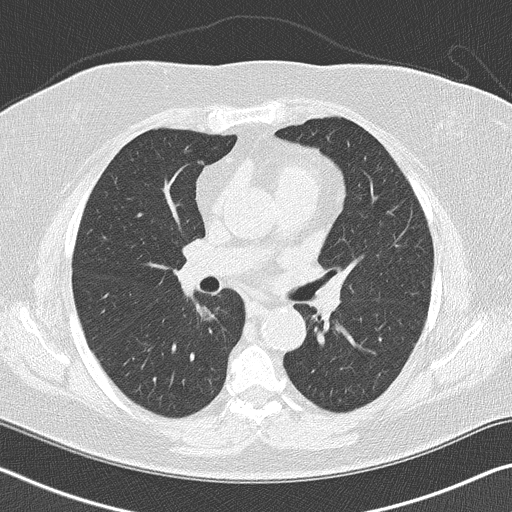
Axial slice from a low-dose chest CT screening exam. First (baseline) screen. Lung window (W 1500 / L -600 HU). 2 mm slice thickness. Female participant, aged 60 years at enrolment.
Expert-annotated lung lesion, box from (x=170, y=291) to (x=228, y=343) px. The screening reader recorded 2 non-calcified nodules or masses ≥4 mm on this exam (right lower lobe, left upper lobe); which of them this box marks is not recorded. Official screen result: positive, change unspecified: nodule(s) >= 4 mm or enlarging nodule(s), mass(es), or other non-specific abnormalities suspicious for lung cancer. Lung cancer was diagnosed 482 days after this screen (after the second annual screen): bronchiolo-alveolar carcinoma, non-mucinous, right lower lobe, stage IA (AJCC 6th edition), 15 mm at pathology.